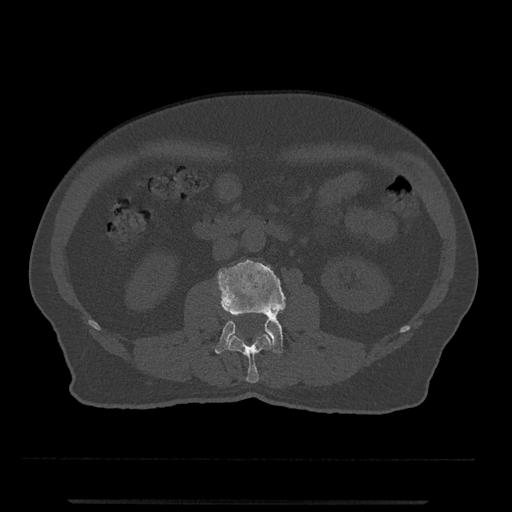
CT including the spine, one axial slice. Position 230 of 797 along the scan axis. 120 kVp. Bone window (W 1800 / L 400 HU). 0.5 mm slice thickness. 512 × 512 image matrix, field of view 419 × 419 mm. Male patient, age 63 years. From the clinical record (not read from this slice): primary cancer: prostate.
Structures marked on this image (semi-automatic segmentation, software-assisted and operator-edited):
- L2 vertebra: bounding box [x1, y1, x2, y2] px = [226, 333, 272, 383]
- L3 vertebra: [215, 259, 288, 354]